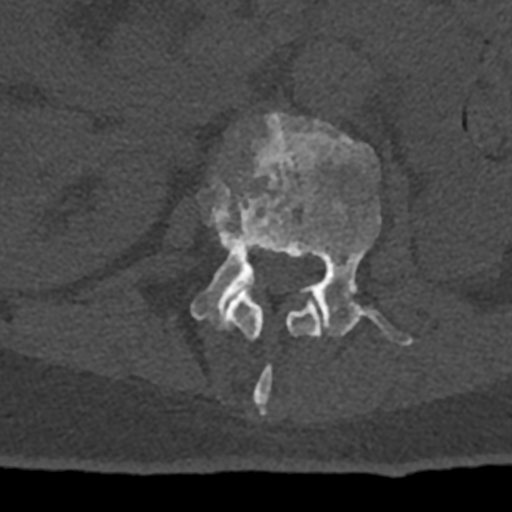
CT including the spine, one axial slice. Slice 400 of 797 in the series (ordered by position). Bone window (W 1800 / L 400 HU). 0.5 mm slice thickness. 512 × 512 image matrix, field of view 160 × 160 mm. Patient: male, 74 years. From the clinical record (not read from this slice): primary cancer: renal; vertebrae with lytic lesions (as recorded): T10, L1, L2, L3, L4, L5.
Annotated regions visible in this slice (semi-automatic segmentation, software-assisted and operator-edited):
- L1 vertebra: bounding box (x1, y1, x2, y2) in pixels: (202, 152, 321, 416)
- L2 vertebra: (190, 111, 413, 346)